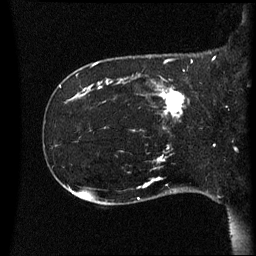
Breast MRI (dynamic contrast-enhanced), one sagittal slice; slice 13 of 60 in the series (ordered by position); dynamic contrast-enhanced series, image 2 of 3 at this slice position (ordered by acquisition); 1.5 T; TE 4.2 ms, TR 8.4 ms; 2.2 mm slice thickness; 256 × 256 image matrix. Patient: female, 41 years. From the clinical record (not read from this slice): setting: breast cancer imaged before/during neoadjuvant chemotherapy; receptor status: HER2-positive.
Annotated regions visible in this slice (semi-automatic segmentation, software-assisted and operator-edited):
- analysis volume of interest (the breast-tissue region the enhancement analysis was run in; not a lesion): bounding box <122,80,193,123> (left, top, right, bottom; pixels)
- tumour enhancement mask (voxels above the 70 % enhancement threshold inside the analysis volume of interest): <157,88,185,119>